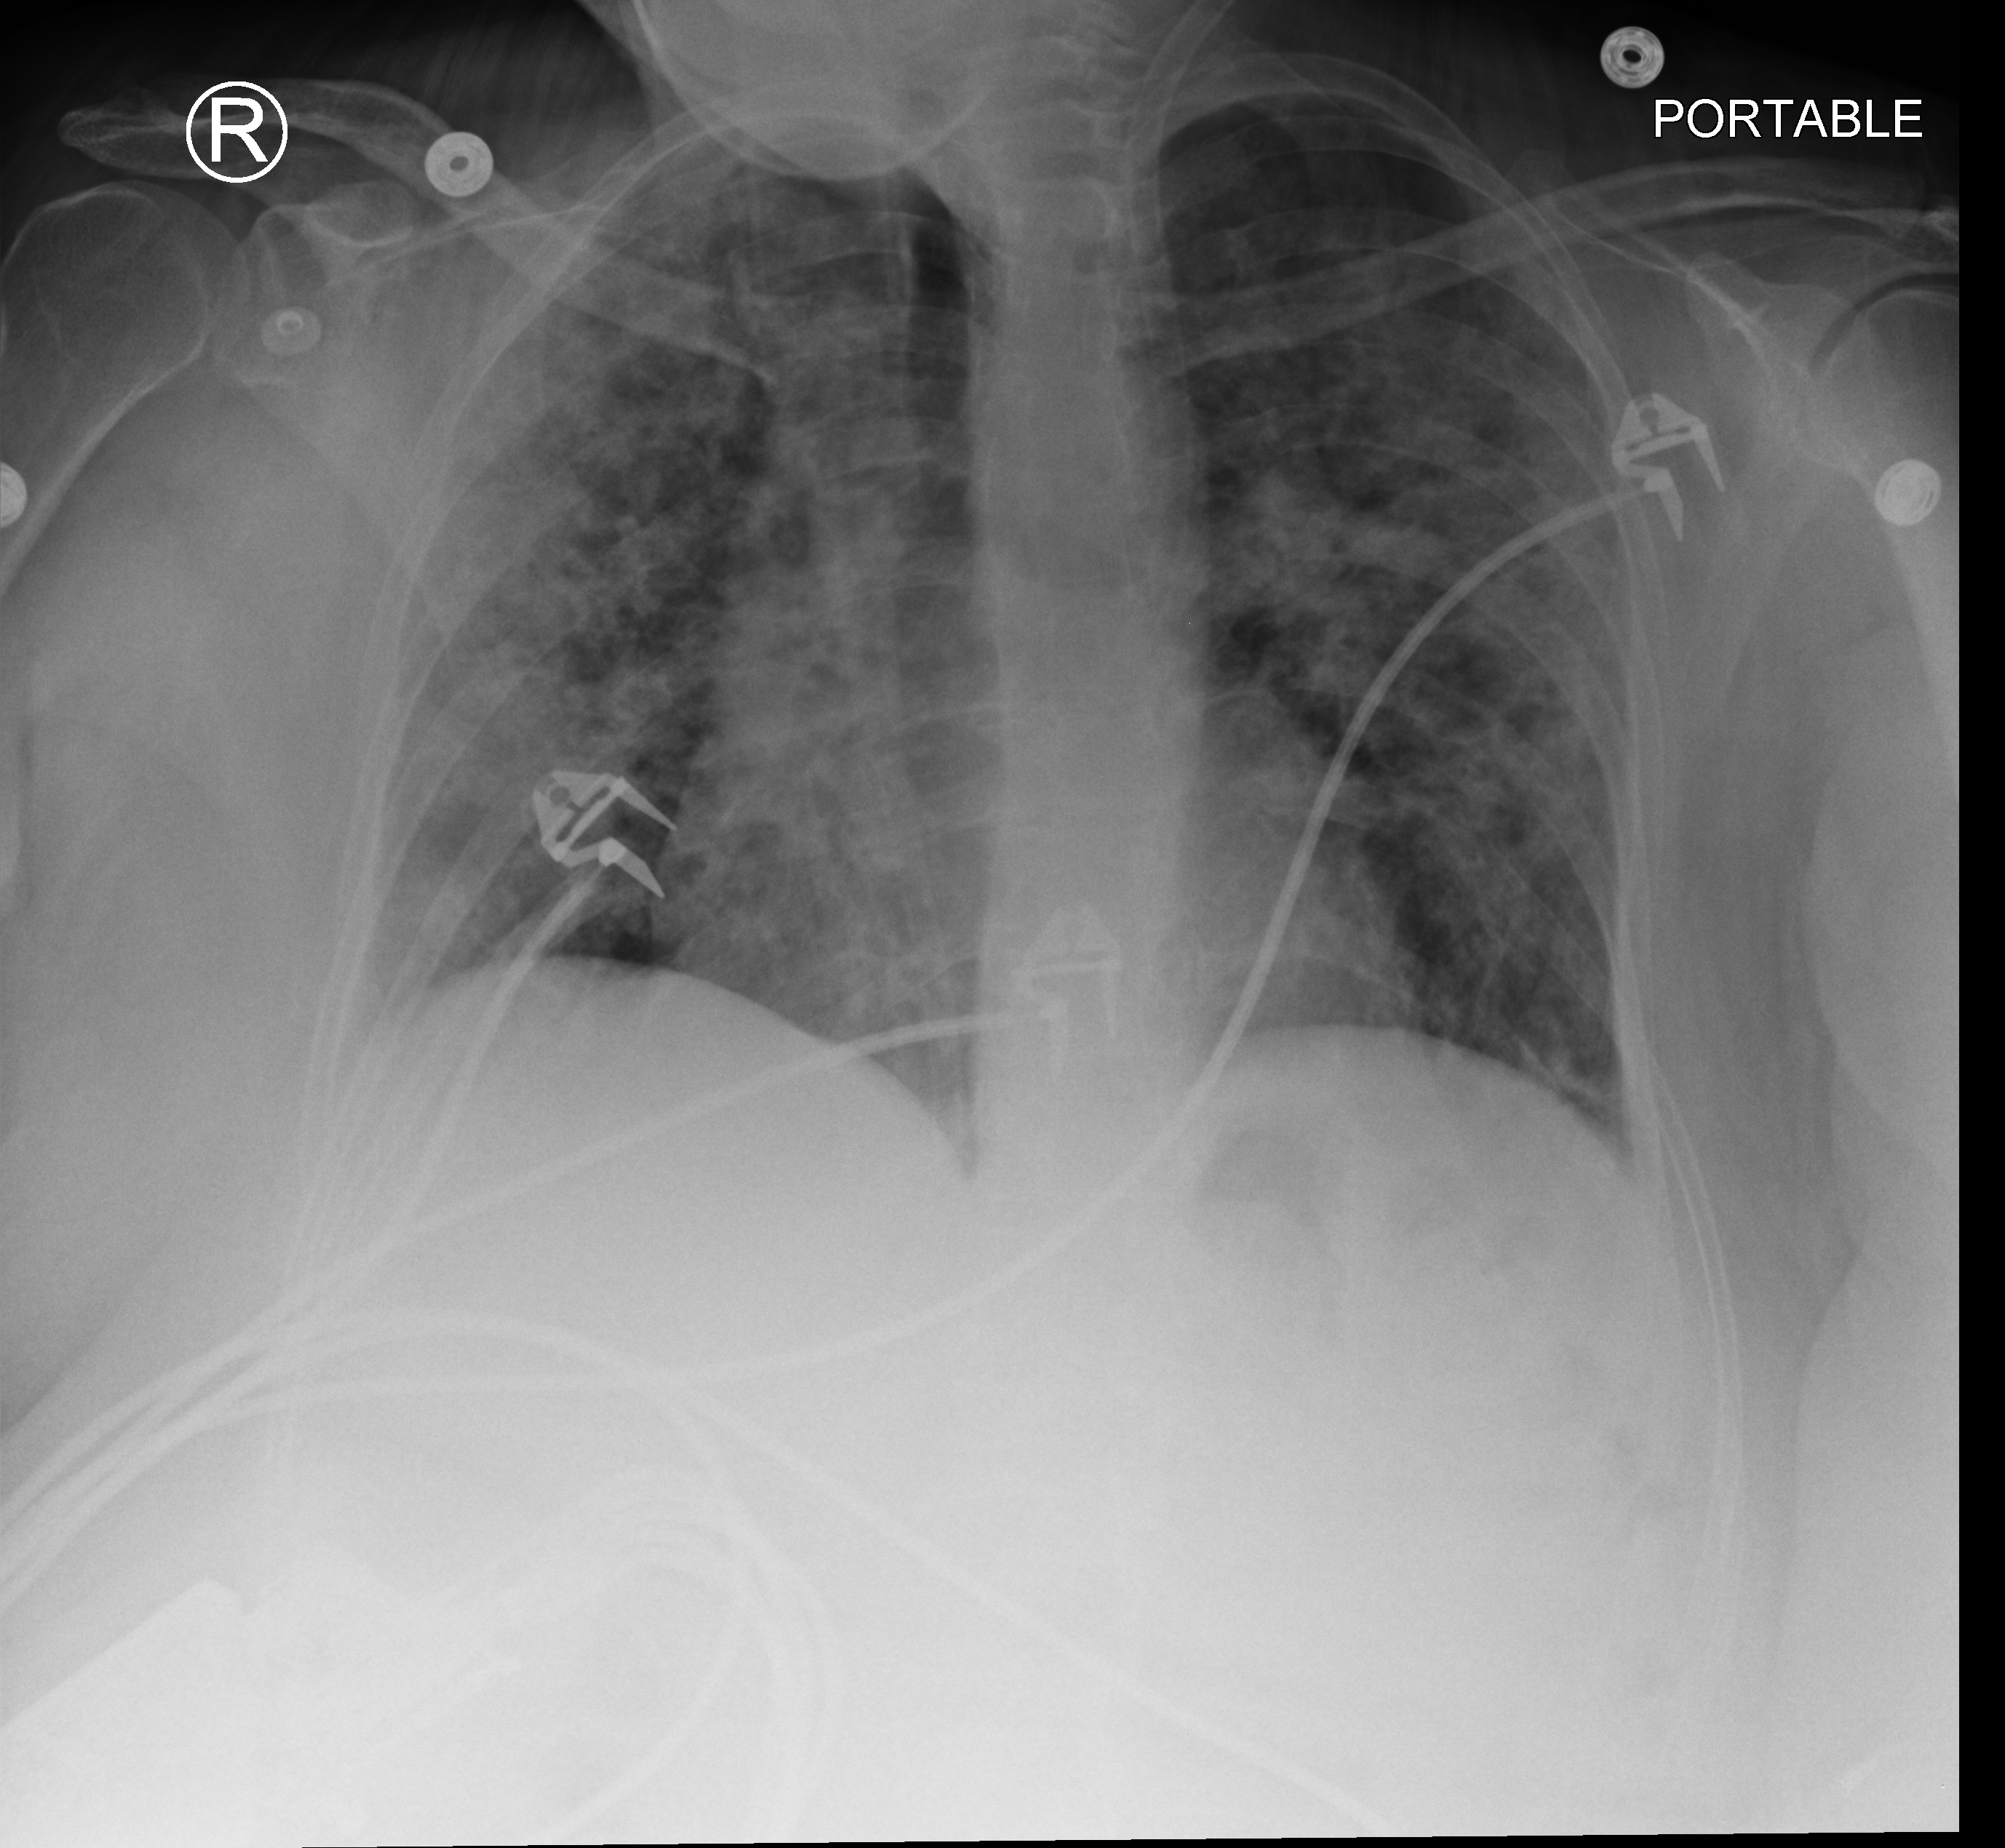
Chest X-ray (portable), anteroposterior (AP) projection. Patient hospitalised with COVID-19; female, aged 18–59 years.
Hospital-stay facts (about this admission, not read from this image; timing relative to this image not recorded): length of hospital stay: 11 days.